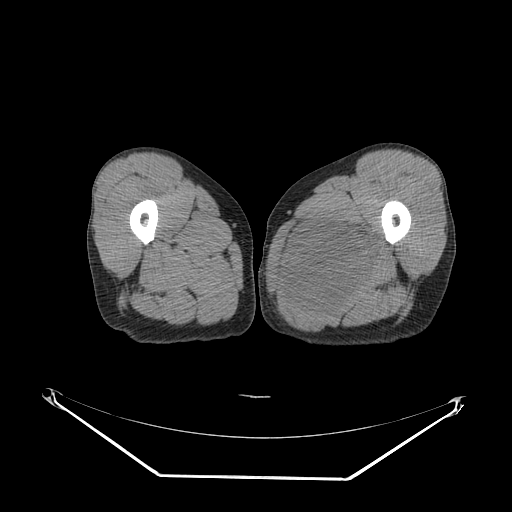
CT of an extremity soft-tissue mass (from a PET/CT study), one axial slice. Position 25 of 267 along the scan axis. Reconstruction kernel SOFT. Soft-tissue window (W 400 / L 40 HU). 3.75 mm slice thickness. 512 × 512 image matrix, field of view 500 × 500 mm. Male patient. Case-level facts recorded for this patient, not image findings: histological type: pleiomorphic liposarcoma; grade: high; site of the primary tumour: left thigh.
Outlined on this slice (expert contour drawn on MRI and transferred to this co-registered scan by the dataset authors):
- gross tumour volume including surrounding oedema: bounding box [x1, y1, x2, y2] px = [286, 215, 387, 312]
- gross tumour volume (mass): [290, 219, 373, 305]